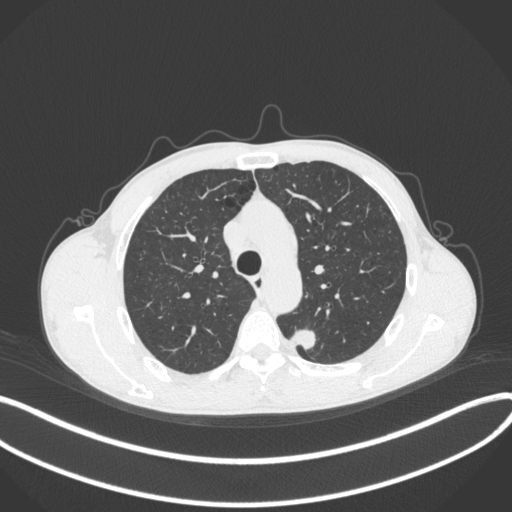
Chest CT, one axial slice. Slice 286 of 429 in the series (ordered by position). Lung window (W 1500 / L -600 HU). 1 mm slice thickness. 512 × 512 image matrix. Male patient, age 51 years. Case-level facts recorded for this patient, not image findings: clinical TNM (as recorded): T2a N1 M1.
Outlined on this slice (rectangle marked by the reading radiologist):
- lung tumour (recorded histology: adenocarcinoma): bounding box [x1, y1, x2, y2] px = [288, 325, 319, 355]